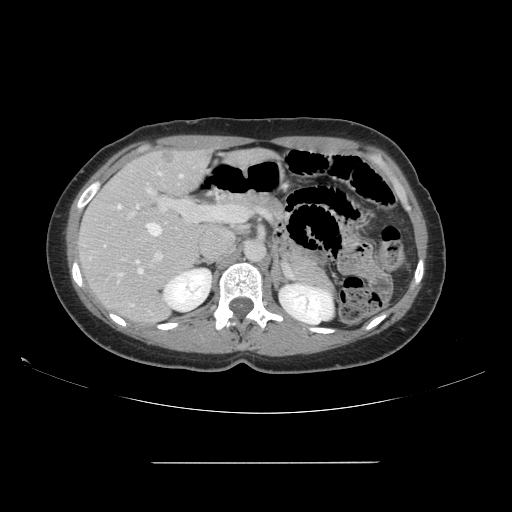
Contrast-enhanced abdominal CT, one axial slice. Position 94 of 151 along the scan axis. 120 kVp. Intravenous contrast given. Soft-tissue window (W 400 / L 40 HU). 512 × 512 image matrix, field of view 421 × 421 mm. Female patient, age 46 years. Case-level facts recorded for this patient, not image findings: diagnosis: colorectal cancer liver metastases, imaged before liver resection; multiple liver metastases: yes; largest metastasis: 3 cm; disease in both lobes: yes.
Structures marked on this image (outlined manually by an expert reader):
- hepatic veins: bounding box <117,172,183,277> (left, top, right, bottom; pixels)
- liver: <80,150,208,323>
- planned liver remnant (the part of the liver to remain after resection): <90,151,209,266>
- portal vein (with intrahepatic branches): <127,182,245,266>
- liver metastasis: <162,153,177,164>